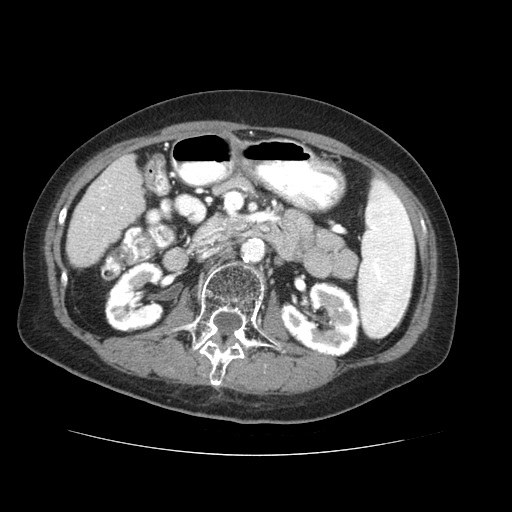
Contrast-enhanced abdominal CT (liver protocol), one axial slice. Position 12 of 73 along the scan axis. Soft-tissue window (W 400 / L 40 HU). 512 × 512 image matrix, field of view 360 × 360 mm. Case-level facts recorded for this patient, not image findings: diagnosis: hepatocellular carcinoma (patient treated with transarterial chemoembolisation; whether this scan precedes or follows treatment is not stated here); TNM stage (as recorded): Stage-IVB; Child-Pugh class: A; tumour differentiation: well differentiated.
Annotated regions visible in this slice (semi-automatically segmented with operator editing):
- liver parenchyma outside the tumour (the mass and vessels are separate outlines, so this box may not span the whole liver): bounding box [x1, y1, x2, y2] px = [66, 154, 144, 266]
- liver vessels: [103, 179, 123, 209]